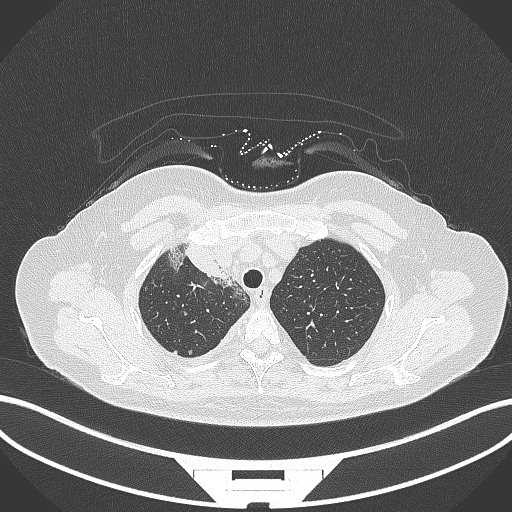
Chest CT, one axial slice; slice 254 of 305 in the series (ordered by position); reconstruction kernel B70f; 120 kVp; lung window (W 1500 / L -600 HU); 512 × 512 image matrix, field of view 400 × 400 mm. Female patient, age 52 years. From the clinical record (not read from this slice): clinical TNM (as recorded): T3 N1 M1.
Structures marked on this image (bounding box drawn by a radiologist):
- lung tumour (recorded histology: adenocarcinoma): box from (x=169, y=236) to (x=231, y=282) px